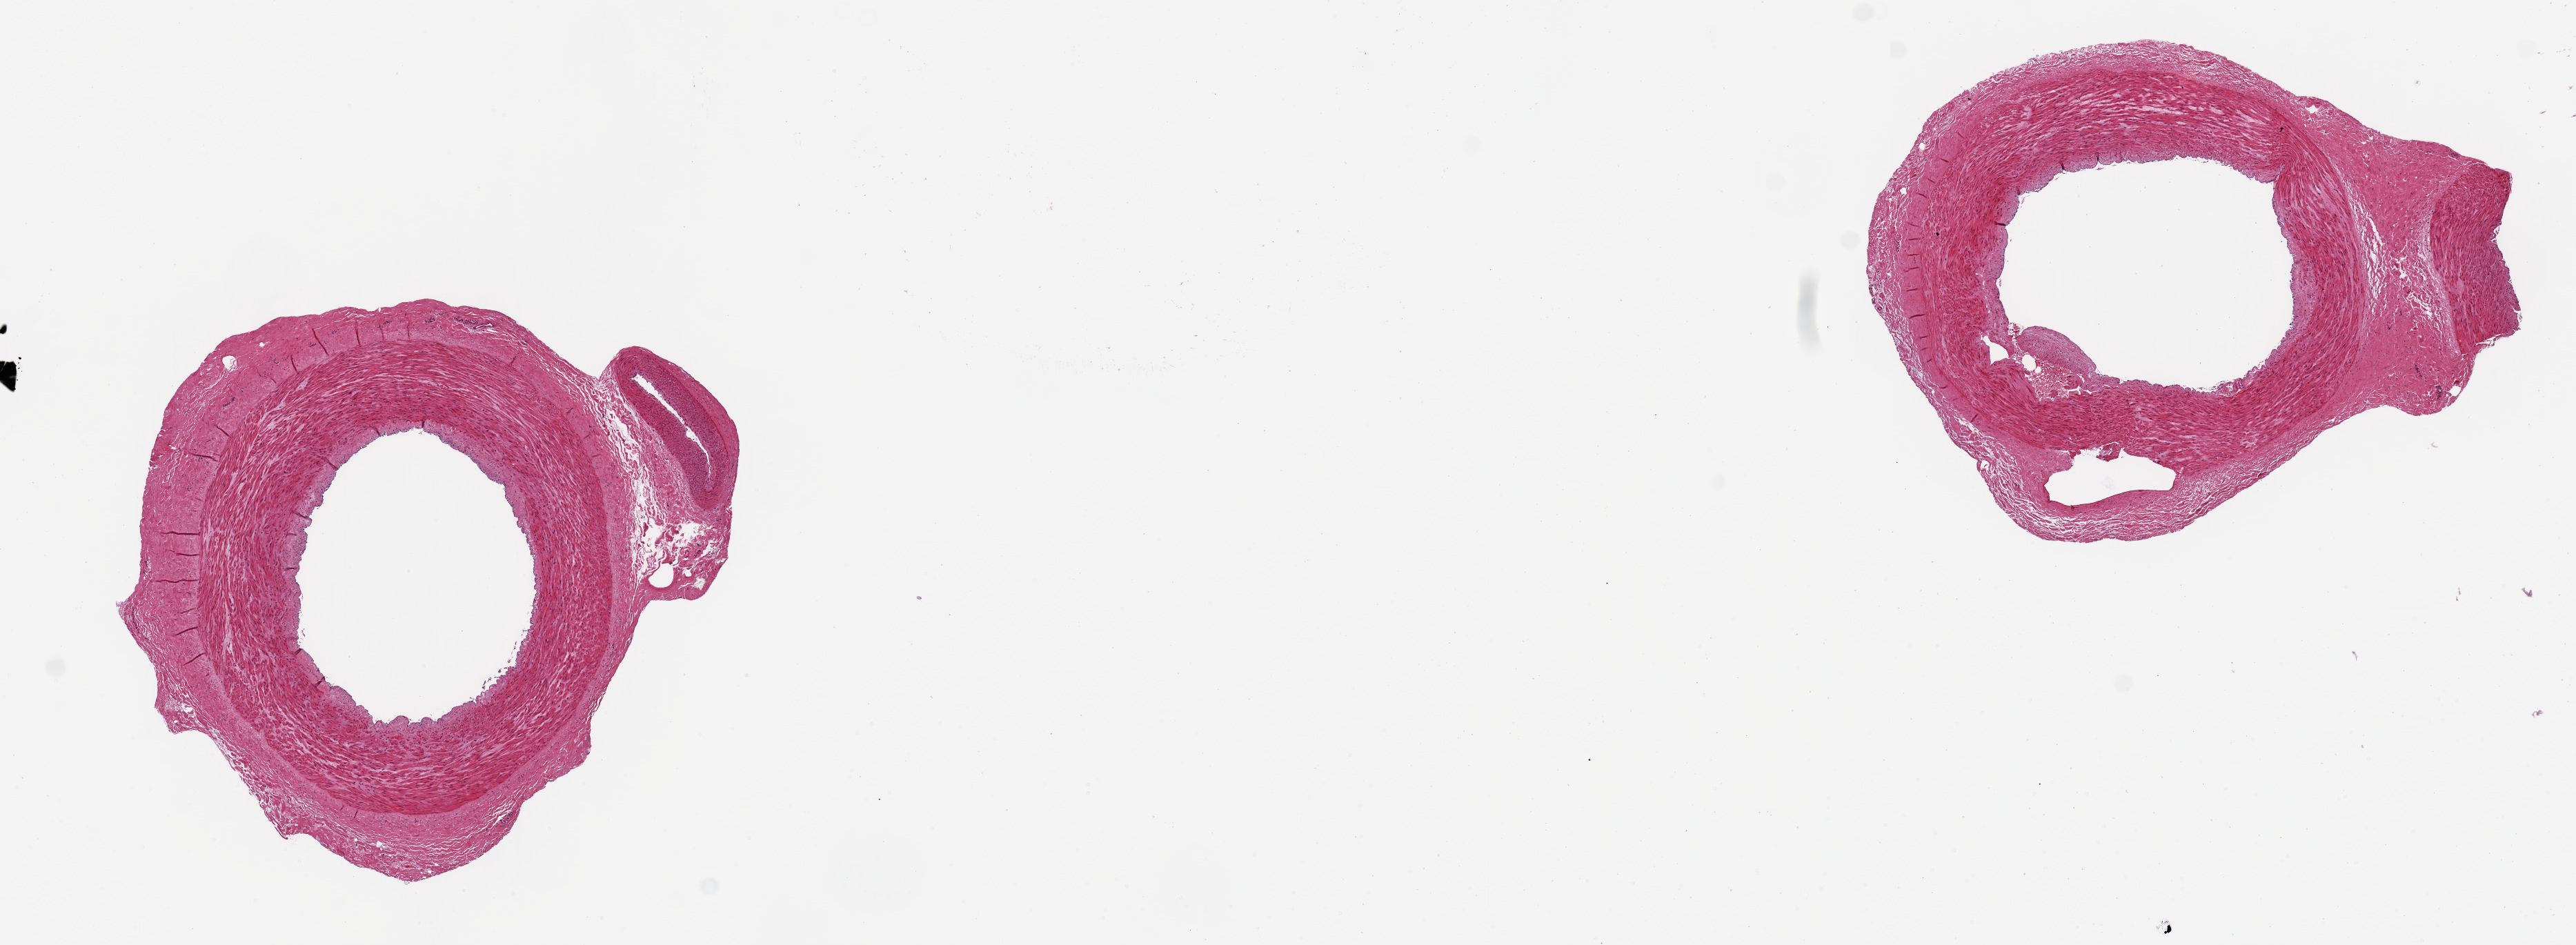
Hematoxylin and eosin (H&E) whole-slide image — whole scanned area (about 14.8 x 5.4 mm) shown as a low-resolution overview. PAXgene-fixed, paraffin-embedded tissue. Target tissue: tibial artery. Tissue donor sample. Male donor.
* pathologist's review note for this sample: 2 pieces ~3mm d. Clean specimens